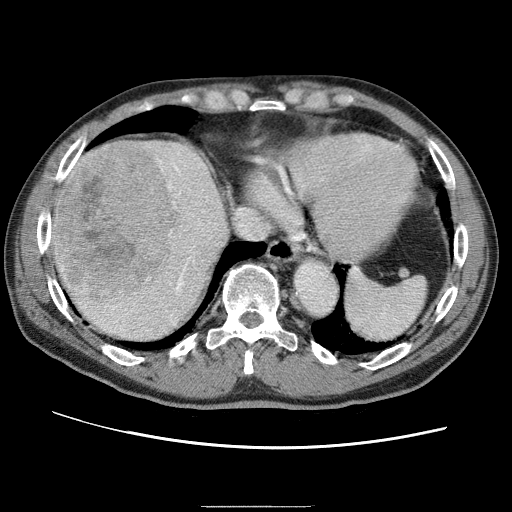
Contrast-enhanced abdominal CT (liver protocol), one axial slice. Position 57 of 75 along the scan axis. Reconstruction kernel STANDARD. One of 2 acquisitions stored at this slice position. Soft-tissue window (W 400 / L 40 HU). 2.5 mm slice thickness. 512 × 512 image matrix, field of view 360 × 360 mm. From the clinical record (not read from this slice): diagnosis: hepatocellular carcinoma (patient treated with transarterial chemoembolisation; whether this scan precedes or follows treatment is not stated here); TNM stage (as recorded): Stage-II; Child-Pugh class: A; tumour size: 2 cm.
Annotated regions visible in this slice (semi-automatically segmented with operator editing):
- liver parenchyma outside the tumour (the mass and vessels are separate outlines, so this box may not span the whole liver): box from (x=50, y=138) to (x=232, y=342) px
- mass: (x=55, y=142)–(x=183, y=301)
- liver vessels: (x=60, y=150)–(x=199, y=305)